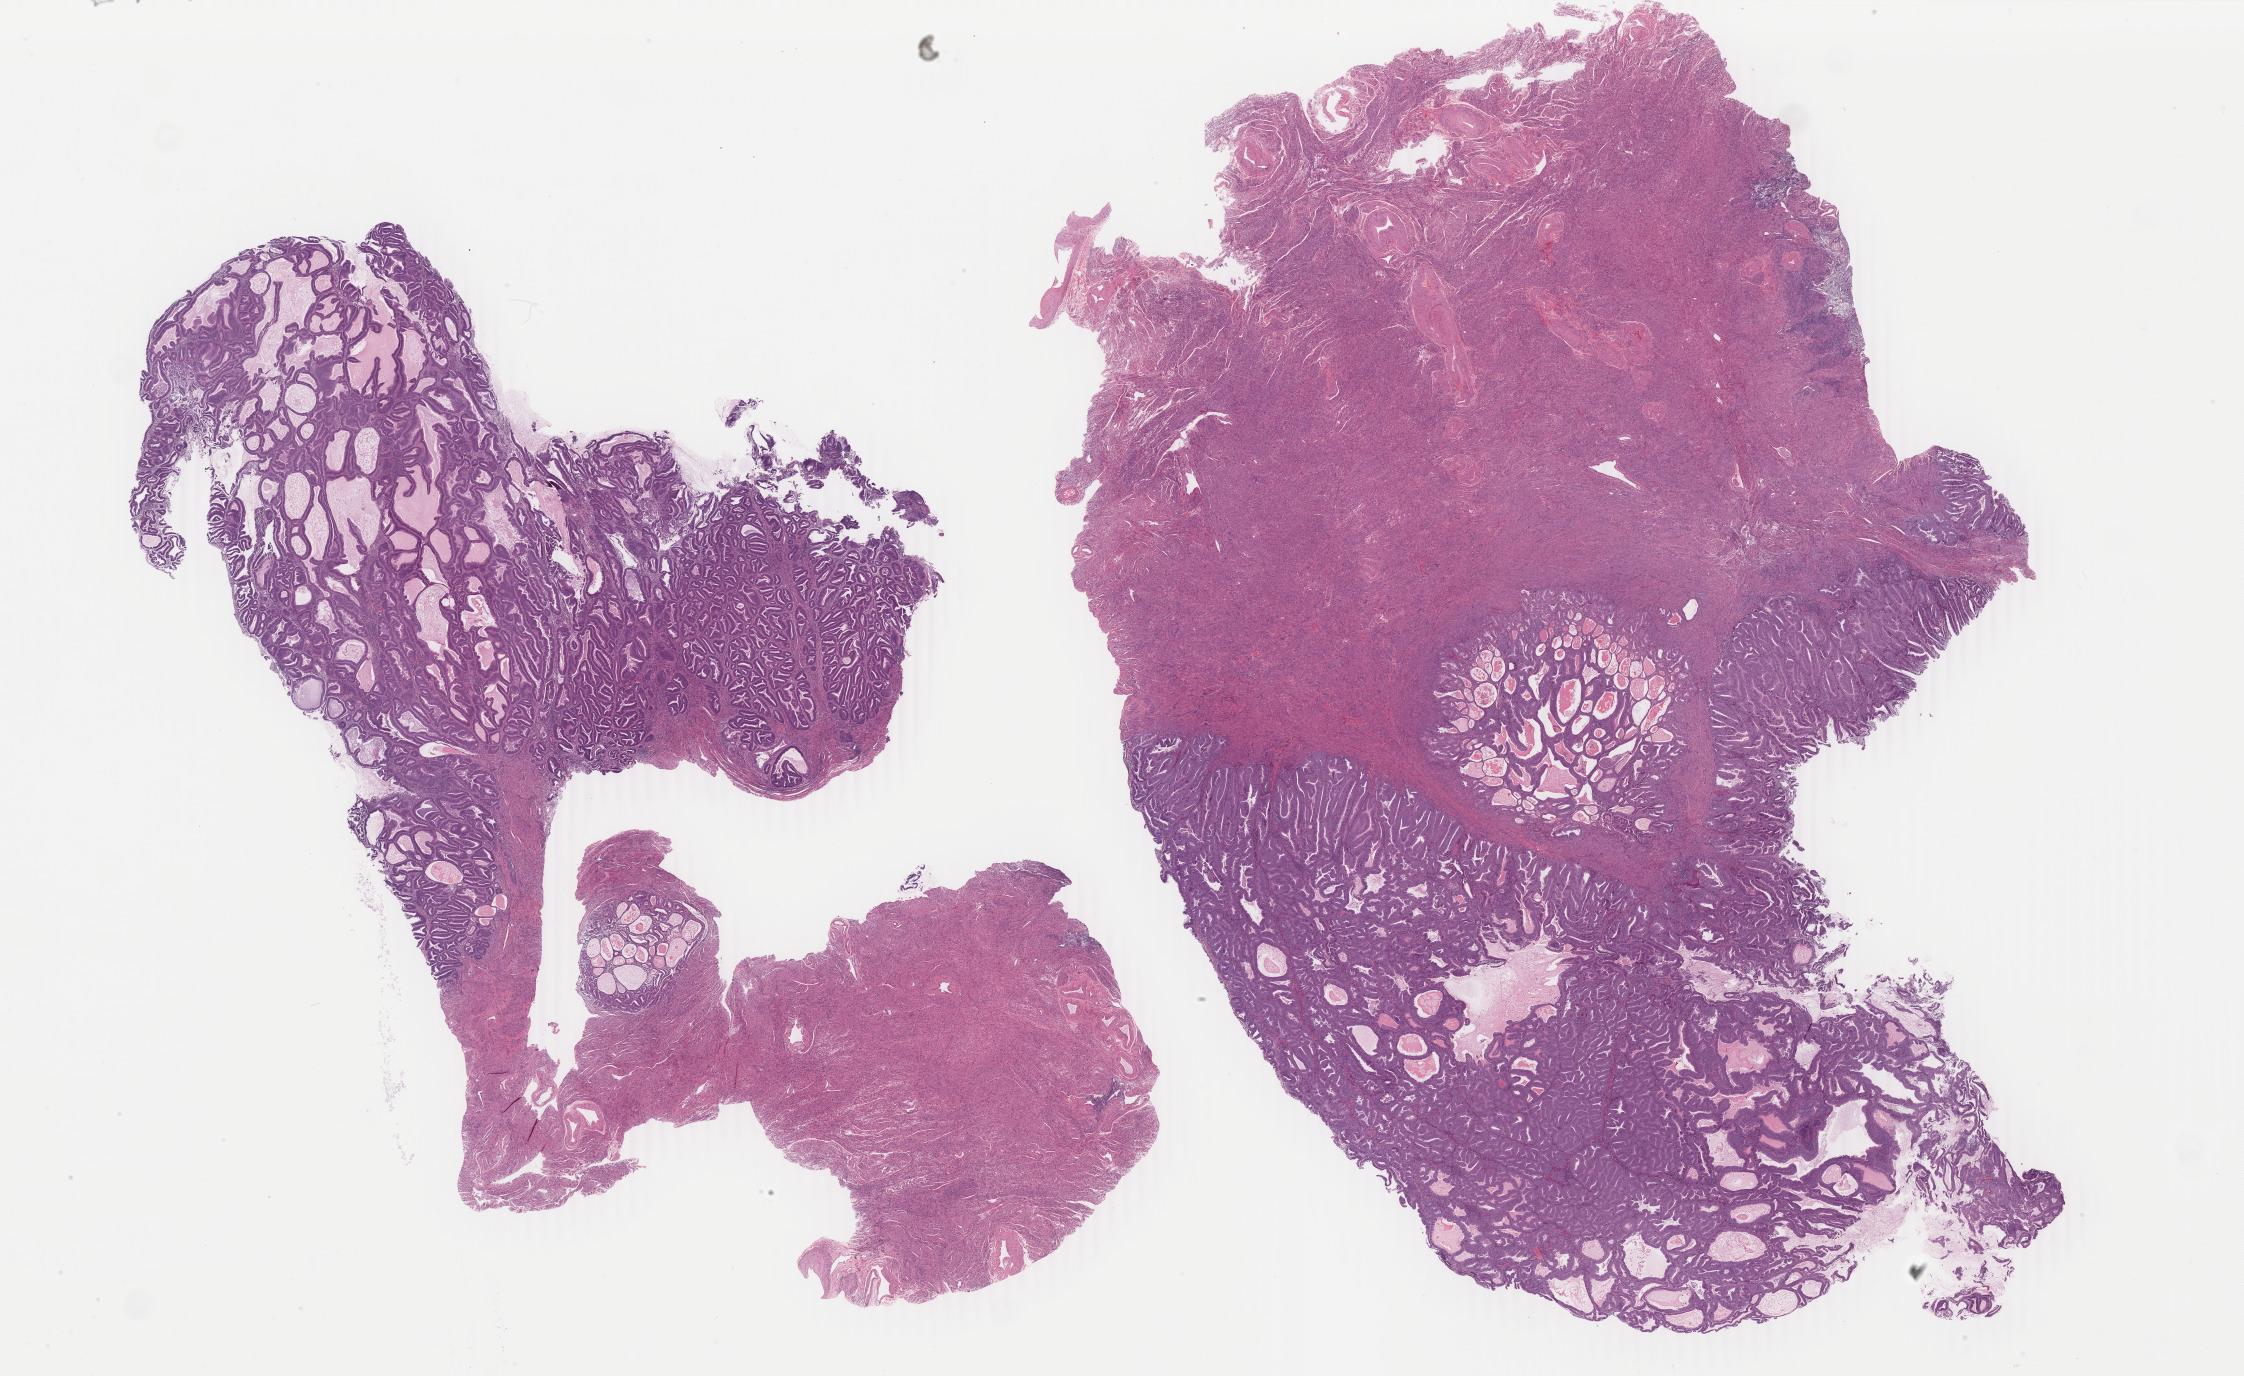
Digitized H&E-stained tissue section (whole slide), a low-resolution overview of the entire scanned area, about 35.7 x 21.9 mm; formalin-fixed paraffin-embedded (FFPE) diagnostic section; primary tumour sample from the uterus. Female patient; age at initial diagnosis 81 years.
Diagnosis: Endometrioid adenocarcinoma, NOS (endometrium).